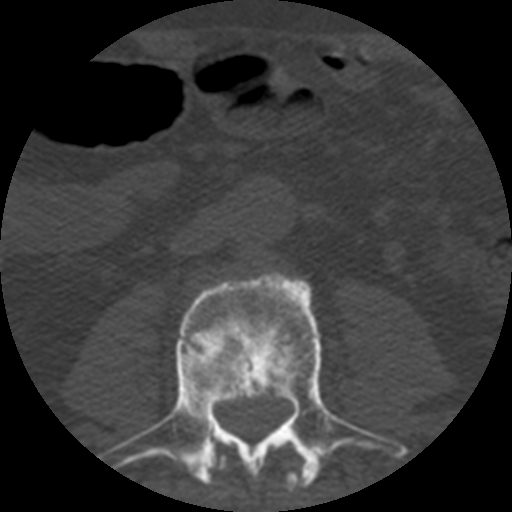
CT including the spine, one axial slice. Slice 123 of 508 in the series (ordered by position). Bone window (W 1800 / L 400 HU). 1.25 mm slice thickness. 512 × 512 image matrix. Patient age 57 years. Case-level facts recorded for this patient, not image findings: primary cancer: prostate.
Outlined on this slice (semi-automatic segmentation, software-assisted and operator-edited):
- L2 vertebra: box from (x=212, y=440) to (x=308, y=491) px
- L3 vertebra: (x=100, y=273)–(x=408, y=485)